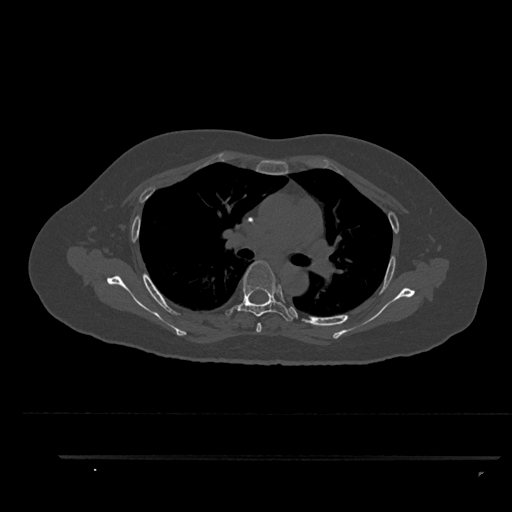
CT including the spine, one axial slice; slice 607 of 797 in the series (ordered by position); reconstruction kernel Br40s/3; 120 kVp; bone window (W 1800 / L 400 HU); 512 × 512 image matrix, field of view 408 × 408 mm. Patient: female, 44 years. Case-level facts recorded for this patient, not image findings: primary cancer: renal.
Outlined on this slice (semi-automatic segmentation, software-assisted and operator-edited):
- T4 vertebra: bounding box (x1, y1, x2, y2) in pixels: (256, 322, 262, 333)
- T5 vertebra: (225, 260, 294, 321)